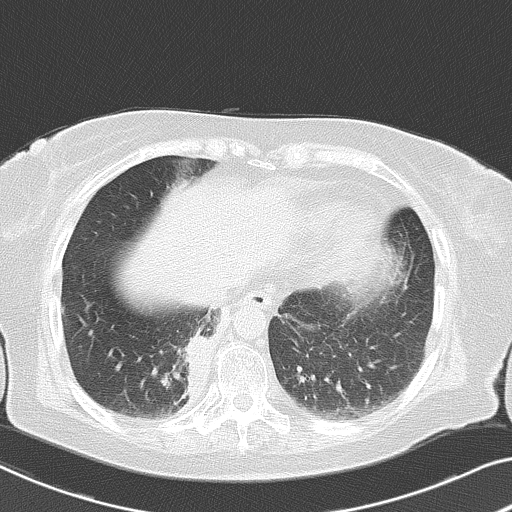
Chest CT, one axial slice. Slice 14 of 53 in the series (ordered by position). Lung window (W 1500 / L -600 HU). 5 mm slice thickness. 512 × 512 image matrix, field of view 333 × 333 mm. Patient: female, 70 years. Case-level facts recorded for this patient, not image findings: clinical TNM (as recorded): T2 N1 M1a.
Annotated regions visible in this slice (rectangle marked by the reading radiologist):
- lung tumour (recorded histology: adenocarcinoma): bounding box [x1, y1, x2, y2] px = [178, 330, 215, 401]